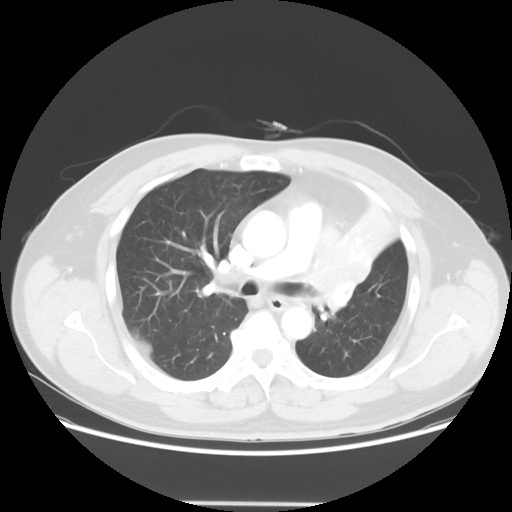
Chest CT, one axial slice. Slice 39 of 62 in the series (ordered by position). Reconstruction kernel STANDARD. 120 kVp. Lung window (W 1500 / L -600 HU). 5 mm slice thickness. 512 × 512 image matrix, field of view 403 × 403 mm. Male patient, age 49 years. Case-level facts recorded for this patient, not image findings: clinical TNM (as recorded): T3 N3 M1c.
Annotated regions visible in this slice (rectangle marked by the reading radiologist):
- lung tumour (recorded histology: squamous cell carcinoma): bounding box <304,229,384,320> (left, top, right, bottom; pixels)